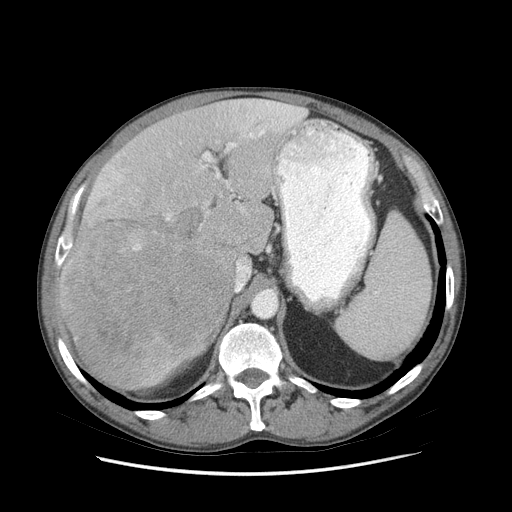
Contrast-enhanced abdominal CT (liver protocol), one axial slice. Position 52 of 89 along the scan axis. Reconstruction kernel STANDARD. Soft-tissue window (W 400 / L 40 HU). 2.5 mm slice thickness. 512 × 512 image matrix, field of view 380 × 380 mm. From the clinical record (not read from this slice): diagnosis: hepatocellular carcinoma (patient treated with transarterial chemoembolisation; whether this scan precedes or follows treatment is not stated here); TNM stage (as recorded): Stage-IIIB; Child-Pugh class: A.
Outlined on this slice (semi-automatically segmented with operator editing):
- liver parenchyma outside the tumour (the mass and vessels are separate outlines, so this box may not span the whole liver): bounding box (x1, y1, x2, y2) in pixels: (56, 98, 304, 390)
- mass: (59, 210, 235, 389)
- liver vessels: (60, 101, 303, 263)